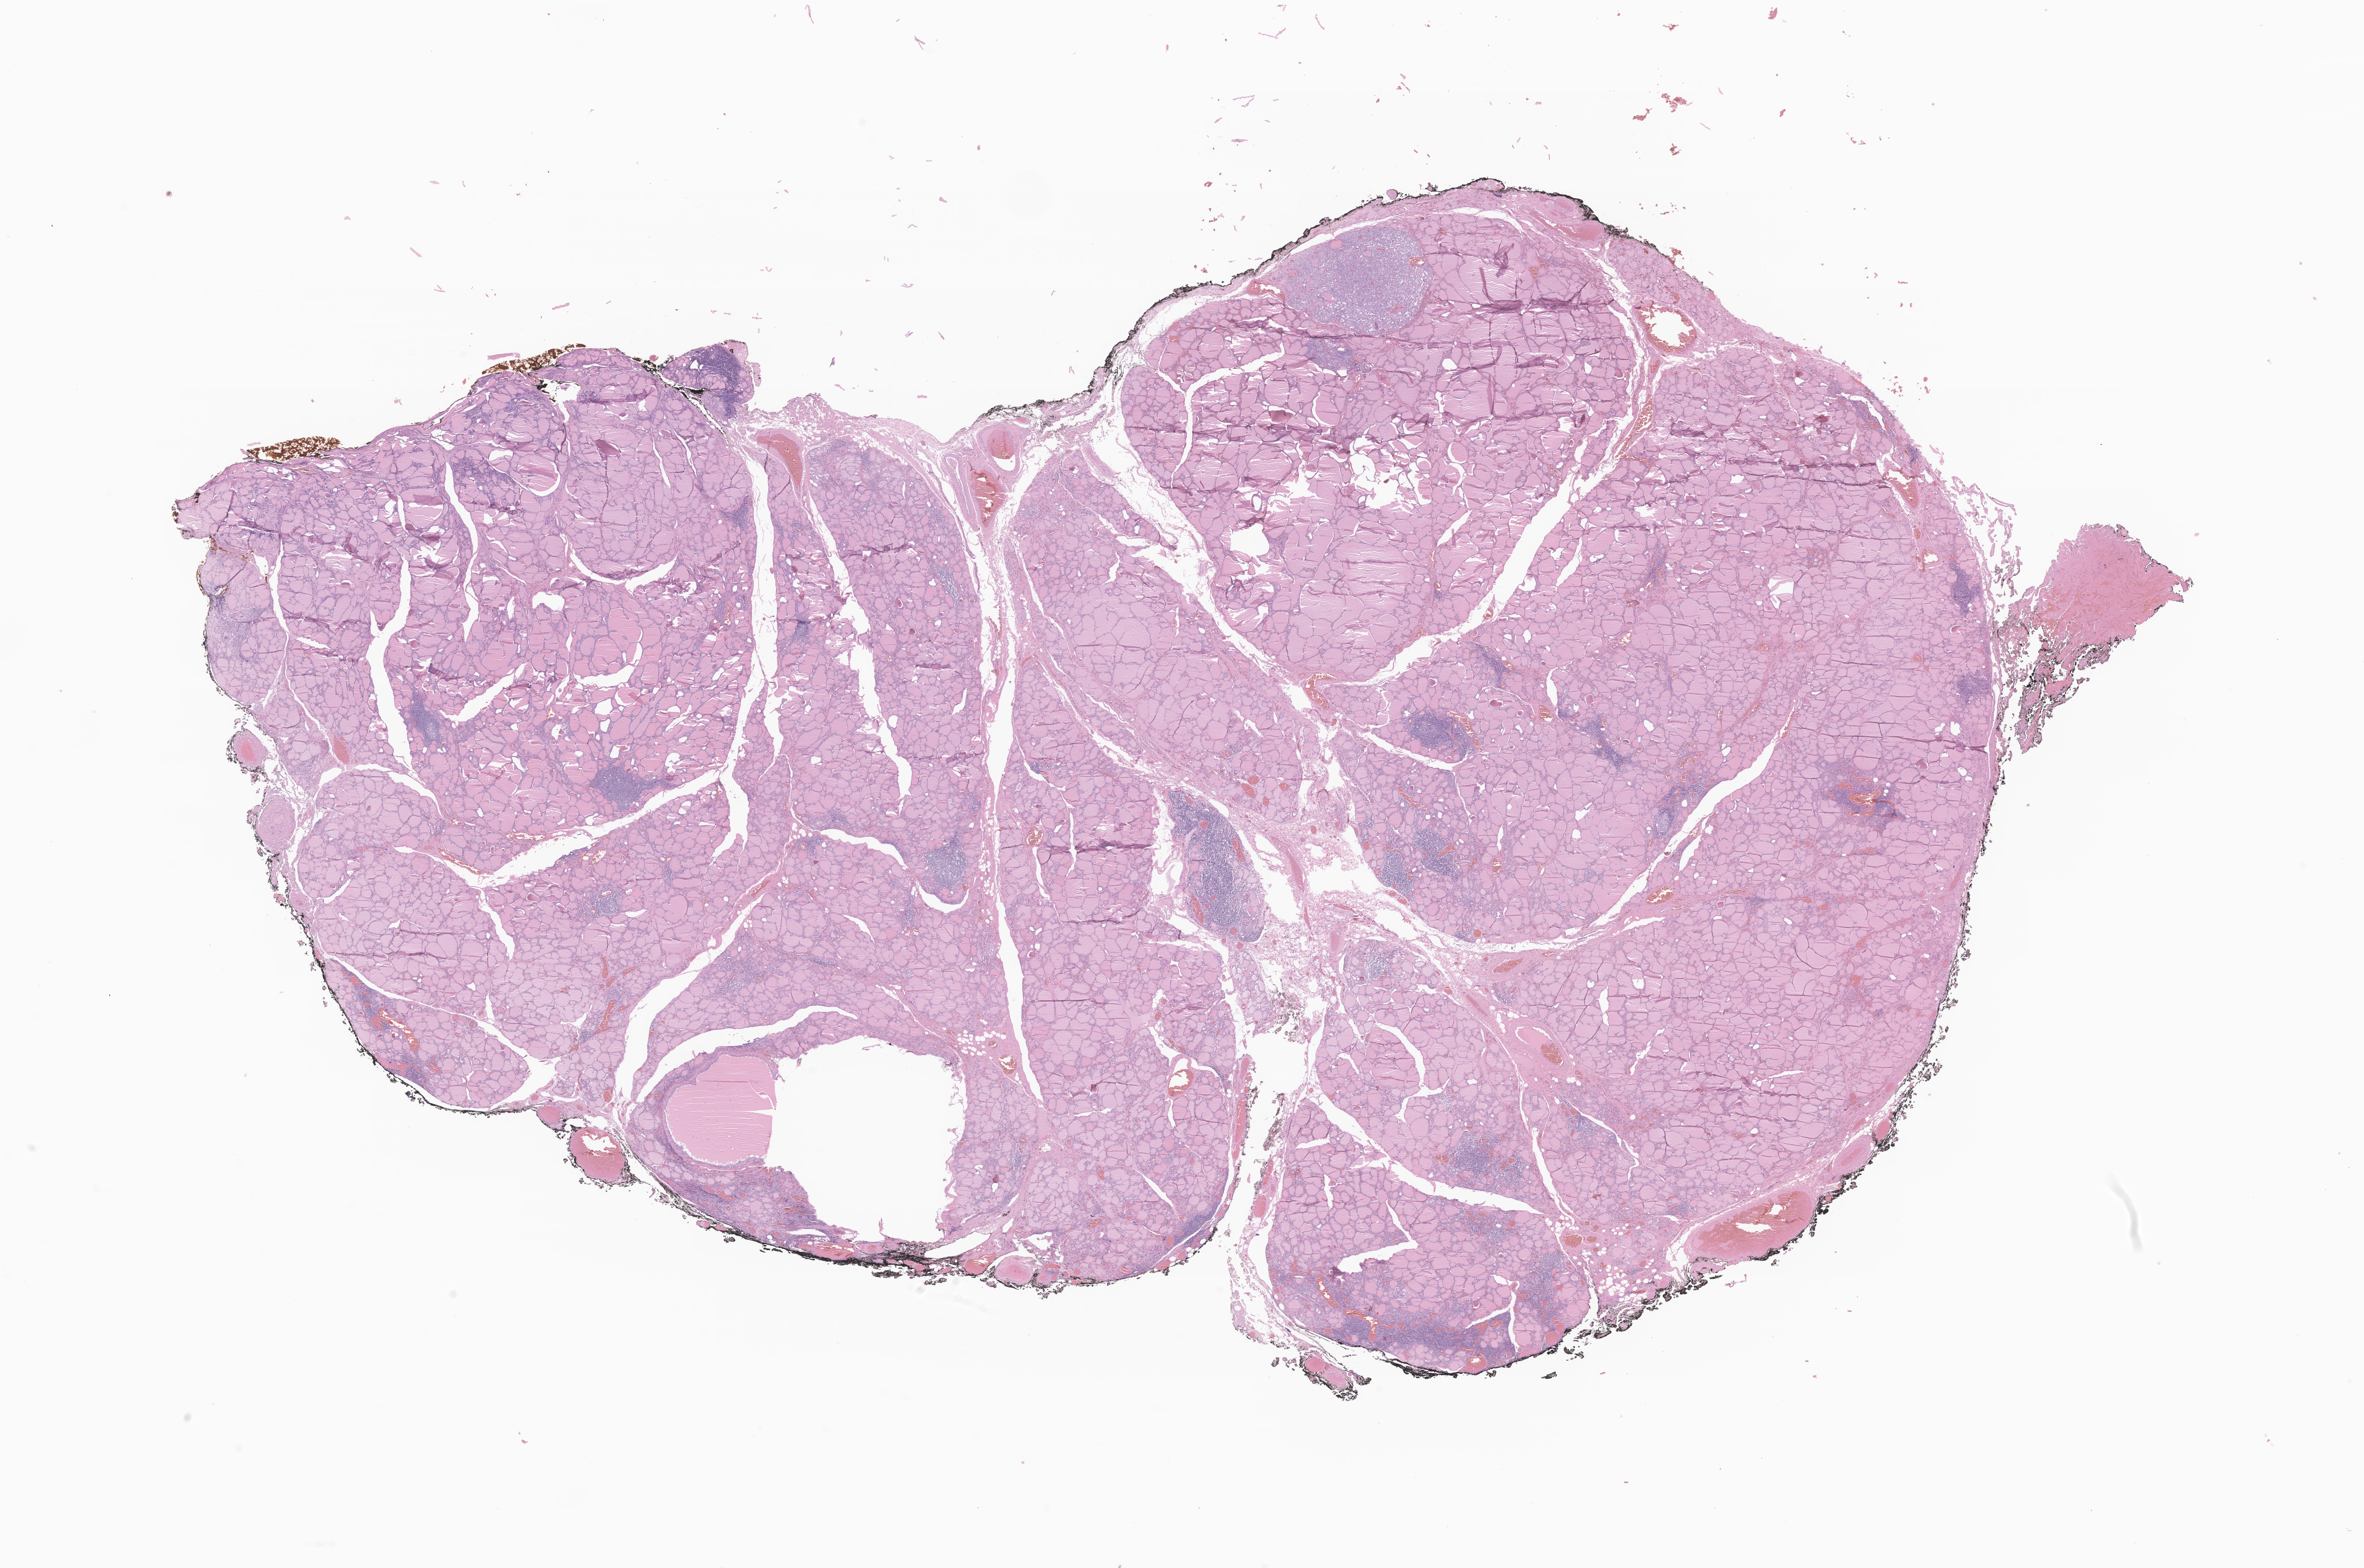
Hematoxylin and eosin (H&E) whole-slide image of tumor tissue from the thyroid, low-resolution overview of the scanned area, about 25.5 x 16.9 mm; formalin-fixed, paraffin-embedded (FFPE) tissue. Patient female; age 202 months (16 years 10 months).
Diagnosis: Papillary carcinoma, NOS.